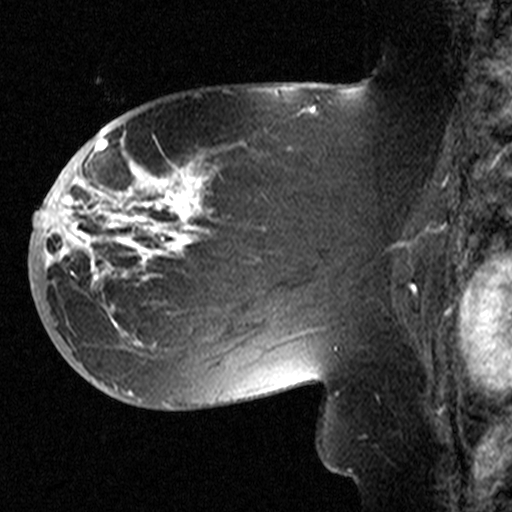
Breast MRI (dynamic contrast-enhanced), one sagittal slice. Dynamic contrast-enhanced study with each time point stored as its own series, time point 2 of 3 at this slice position (early post-contrast, ordered by acquisition time). 1.5 T. TE 4.5 ms, TR 11 ms. 512 × 512 image matrix, field of view 200 × 200 mm. Patient: female, 53 years. Case-level facts recorded for this patient, not image findings: setting: breast cancer imaged before/during neoadjuvant chemotherapy; receptor status: HR-positive, HER2-negative.
Annotated regions visible in this slice (semi-automatically segmented with operator editing):
- analysis volume of interest (the breast-tissue region the enhancement analysis was run in; not a lesion): bounding box (x1, y1, x2, y2) in pixels: (58, 154, 311, 367)
- tumour enhancement mask (voxels above the 90 % enhancement threshold inside the analysis volume of interest): (58, 165, 208, 336)